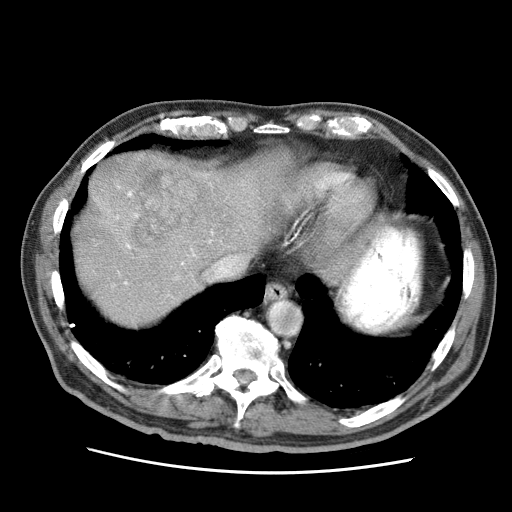
Contrast-enhanced abdominal CT (liver protocol), one axial slice; position 57 of 75 along the scan axis; reconstruction kernel STANDARD; 120 kVp; soft-tissue window (W 400 / L 40 HU); 2.5 mm slice thickness; 512 × 512 image matrix, field of view 360 × 360 mm. From the clinical record (not read from this slice): diagnosis: hepatocellular carcinoma (patient treated with transarterial chemoembolisation; whether this scan precedes or follows treatment is not stated here); TNM stage (as recorded): Stage-IIIA; Child-Pugh class: A; tumour nodularity: multinodular; tumour size: 13.9 cm.
Structures marked on this image (semi-automatically segmented with operator editing):
- liver parenchyma outside the tumour (the mass and vessels are separate outlines, so this box may not span the whole liver): bounding box (x1, y1, x2, y2) in pixels: (74, 150, 288, 324)
- mass: (71, 150, 212, 252)
- liver vessels: (124, 231, 213, 285)